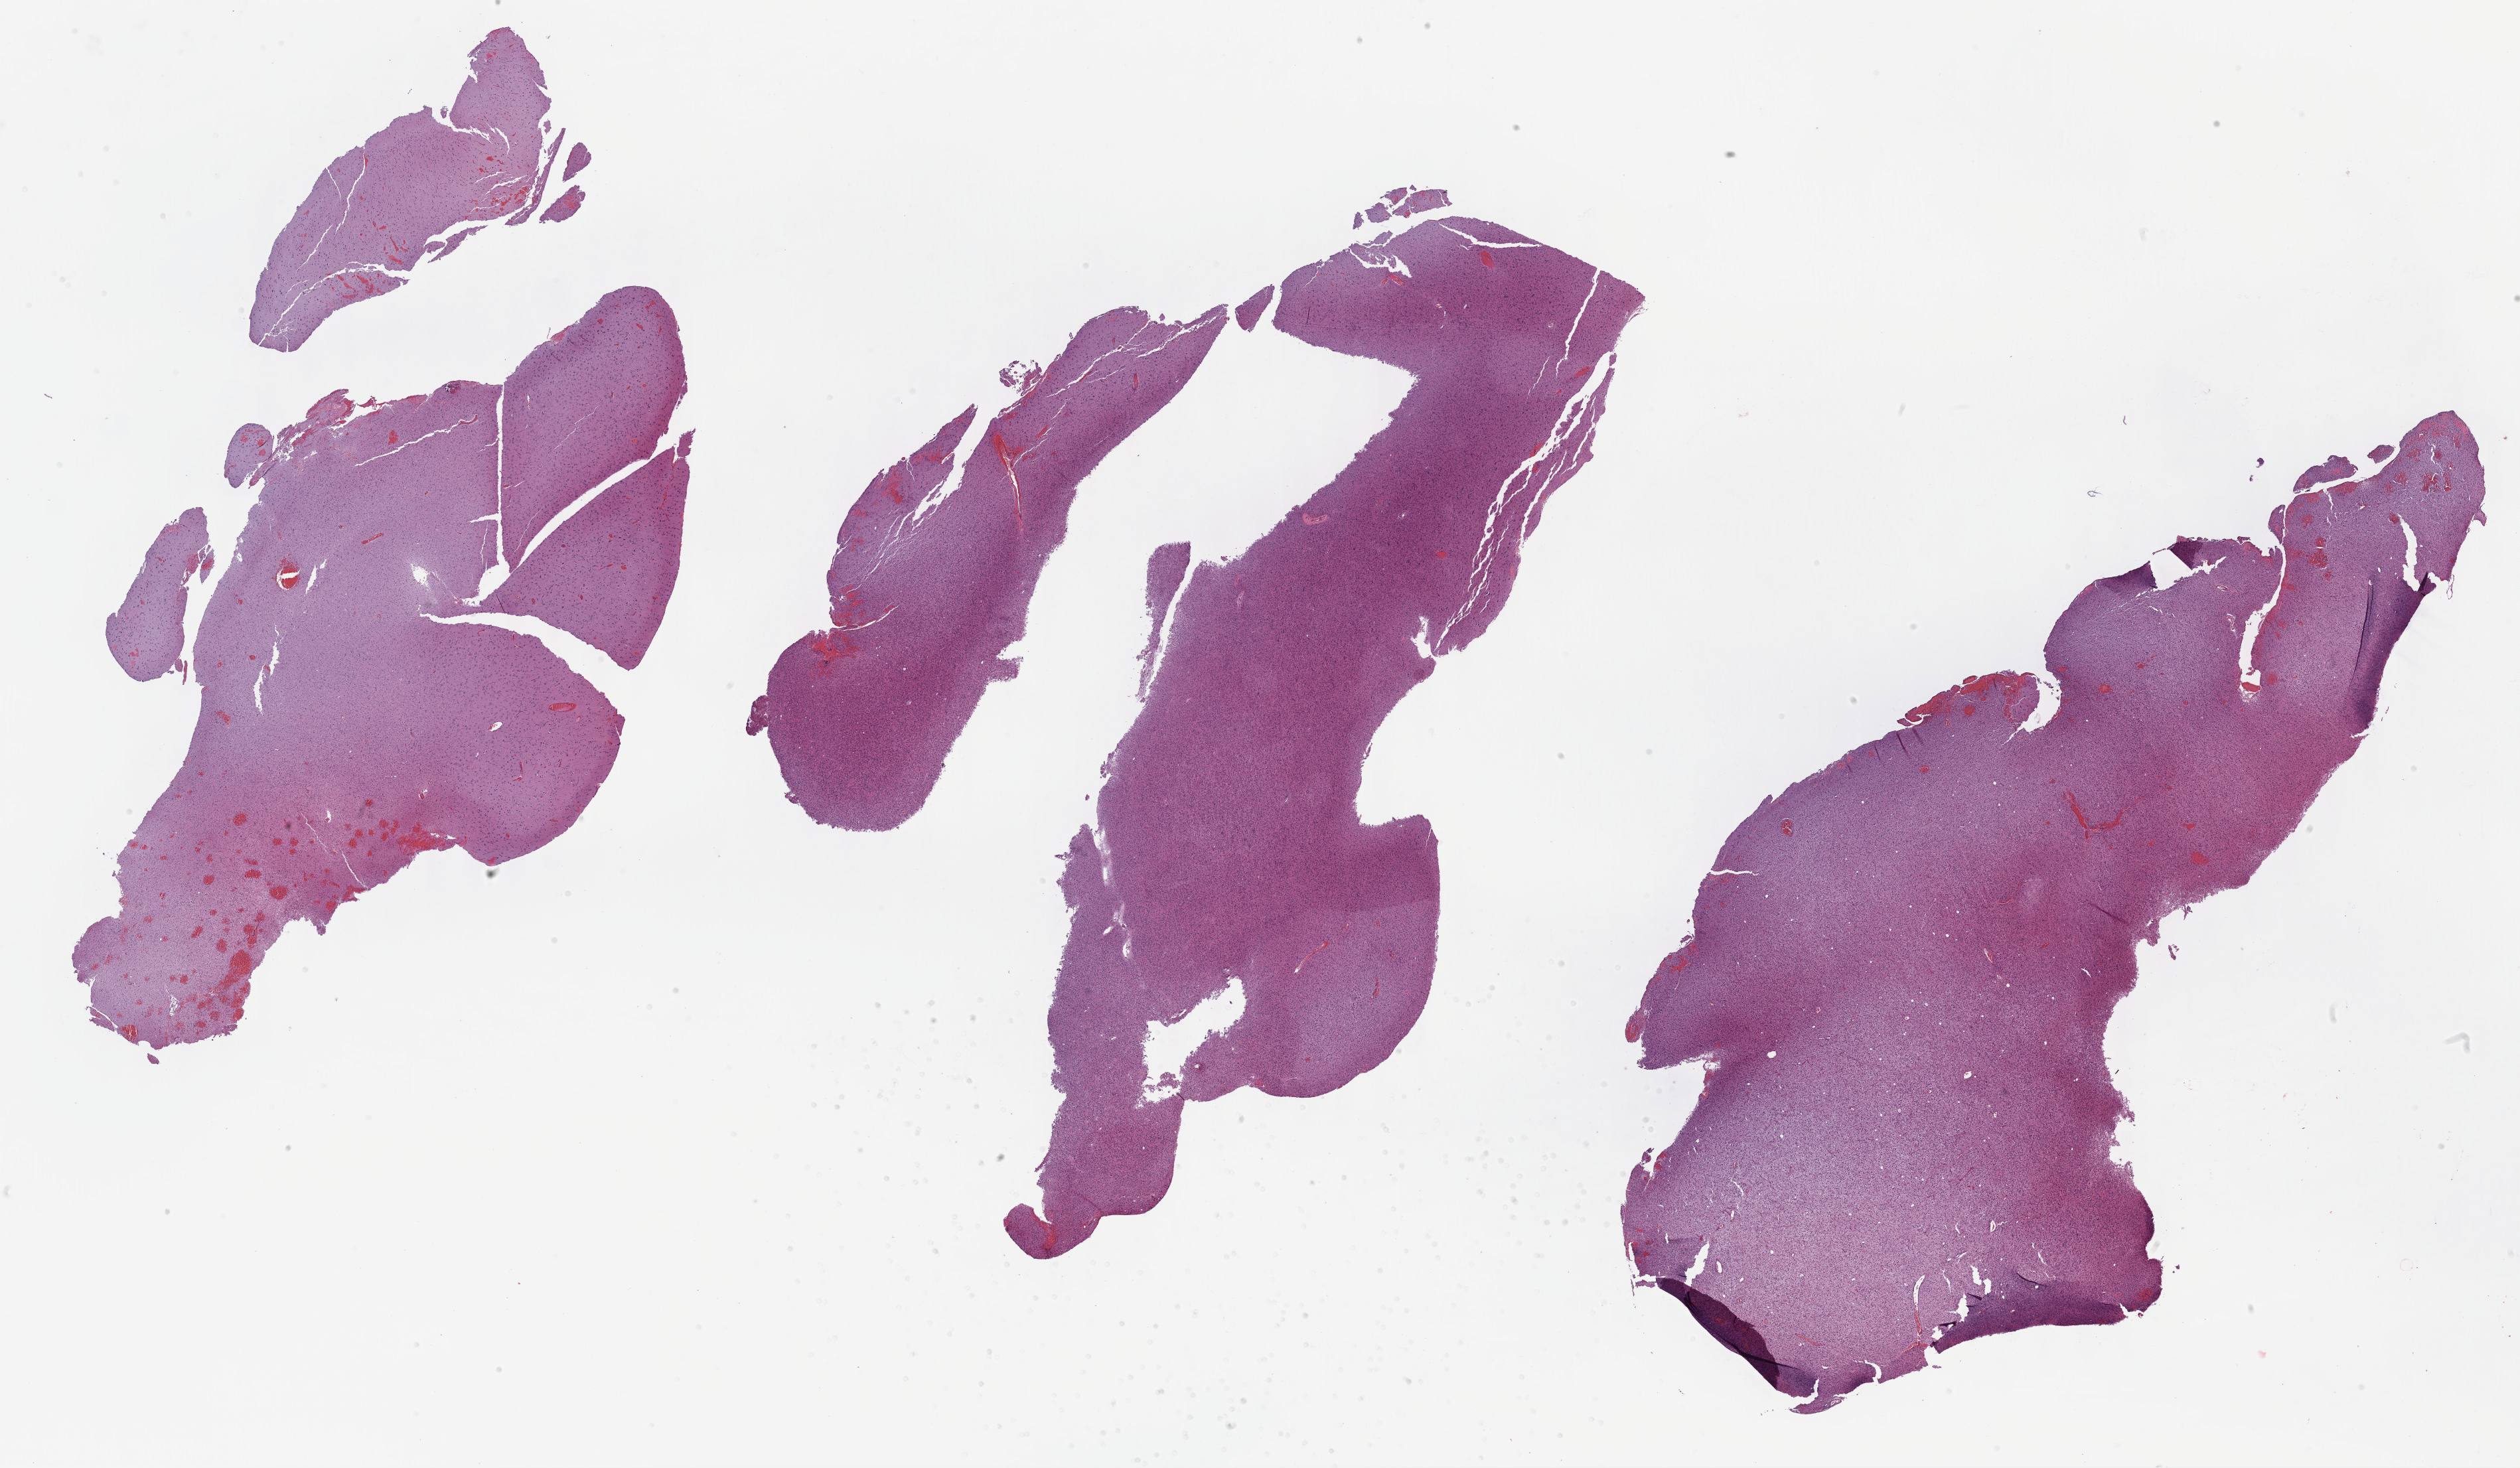
H&E-stained whole-slide image — a low-resolution overview of the entire scanned area, about 30.7 x 17.9 mm (from a 40x scan); formalin-fixed paraffin-embedded (FFPE) diagnostic section; primary tumour sample from the brain. Male, age 25 years at initial diagnosis.
Diagnosis: Oligodendroglioma, NOS (cerebrum).